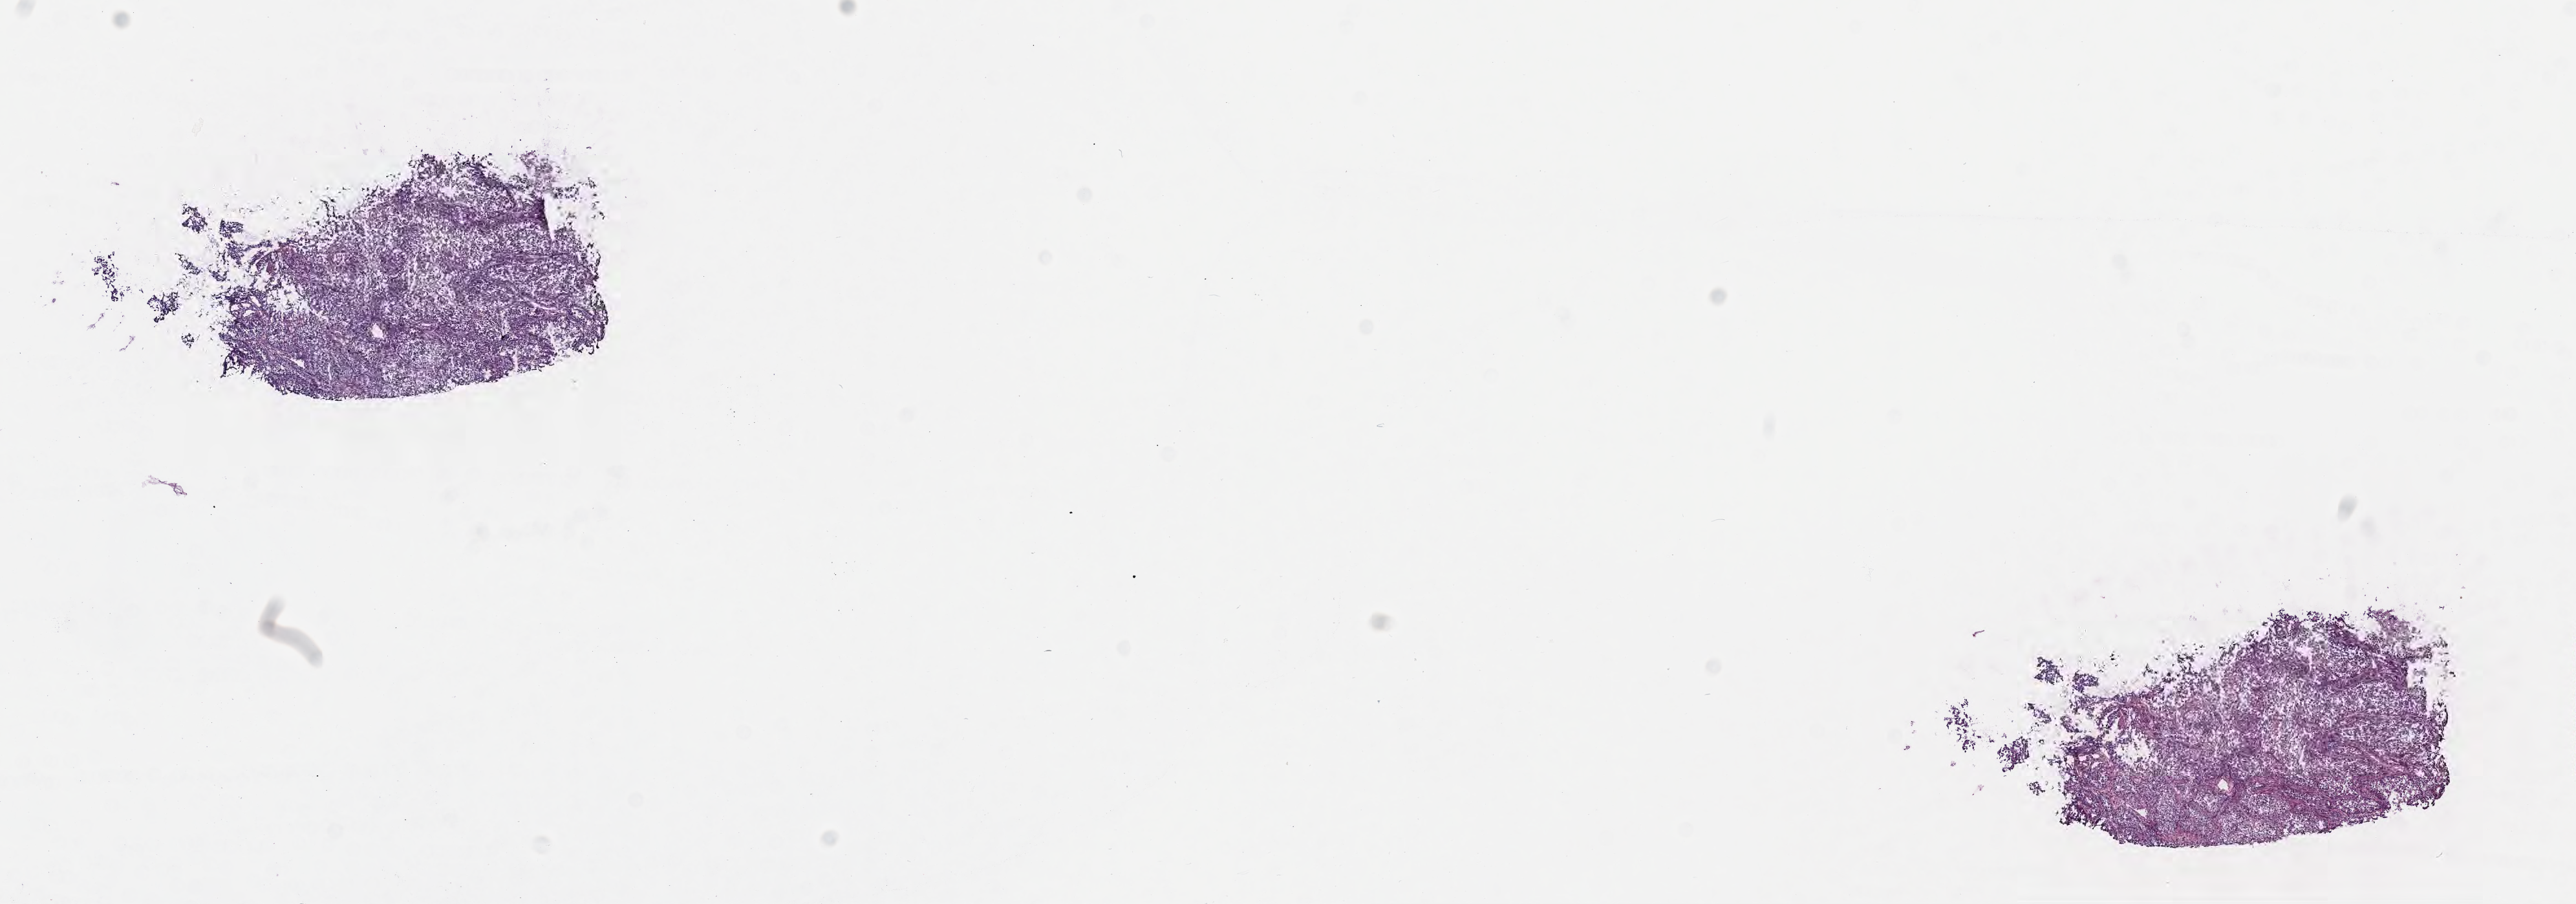
H&E whole-slide image — whole scanned area (about 16.1 x 5.6 mm) shown as a low-resolution overview, frozen section, primary tumor, anatomic site: lower lobe of left lung. Patient male; 64 years old.
Diagnosis: Acinar cell carcinoma.